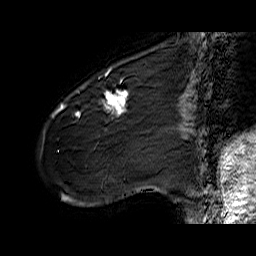
Breast MRI (dynamic contrast-enhanced), one sagittal slice. Slice 16 of 60 in the series (ordered by position). Dynamic contrast-enhanced series, time point 2 of 6 at this slice position (early post-contrast). 1.5 T. TE 6.4 ms, TR 32.9 ms. 4 mm slice thickness. 256 × 256 image matrix, field of view 200 × 200 mm. Female patient. From the clinical record (not read from this slice): setting: breast cancer imaged before/during neoadjuvant chemotherapy; receptor status: HER2-positive.
Annotated regions visible in this slice (semi-automatically segmented with operator editing):
- analysis volume of interest (the breast-tissue region the enhancement analysis was run in; not a lesion): bounding box <61,77,141,142> (left, top, right, bottom; pixels)
- tumour enhancement mask (voxels above the 100 % enhancement threshold inside the analysis volume of interest): <61,80,128,118>